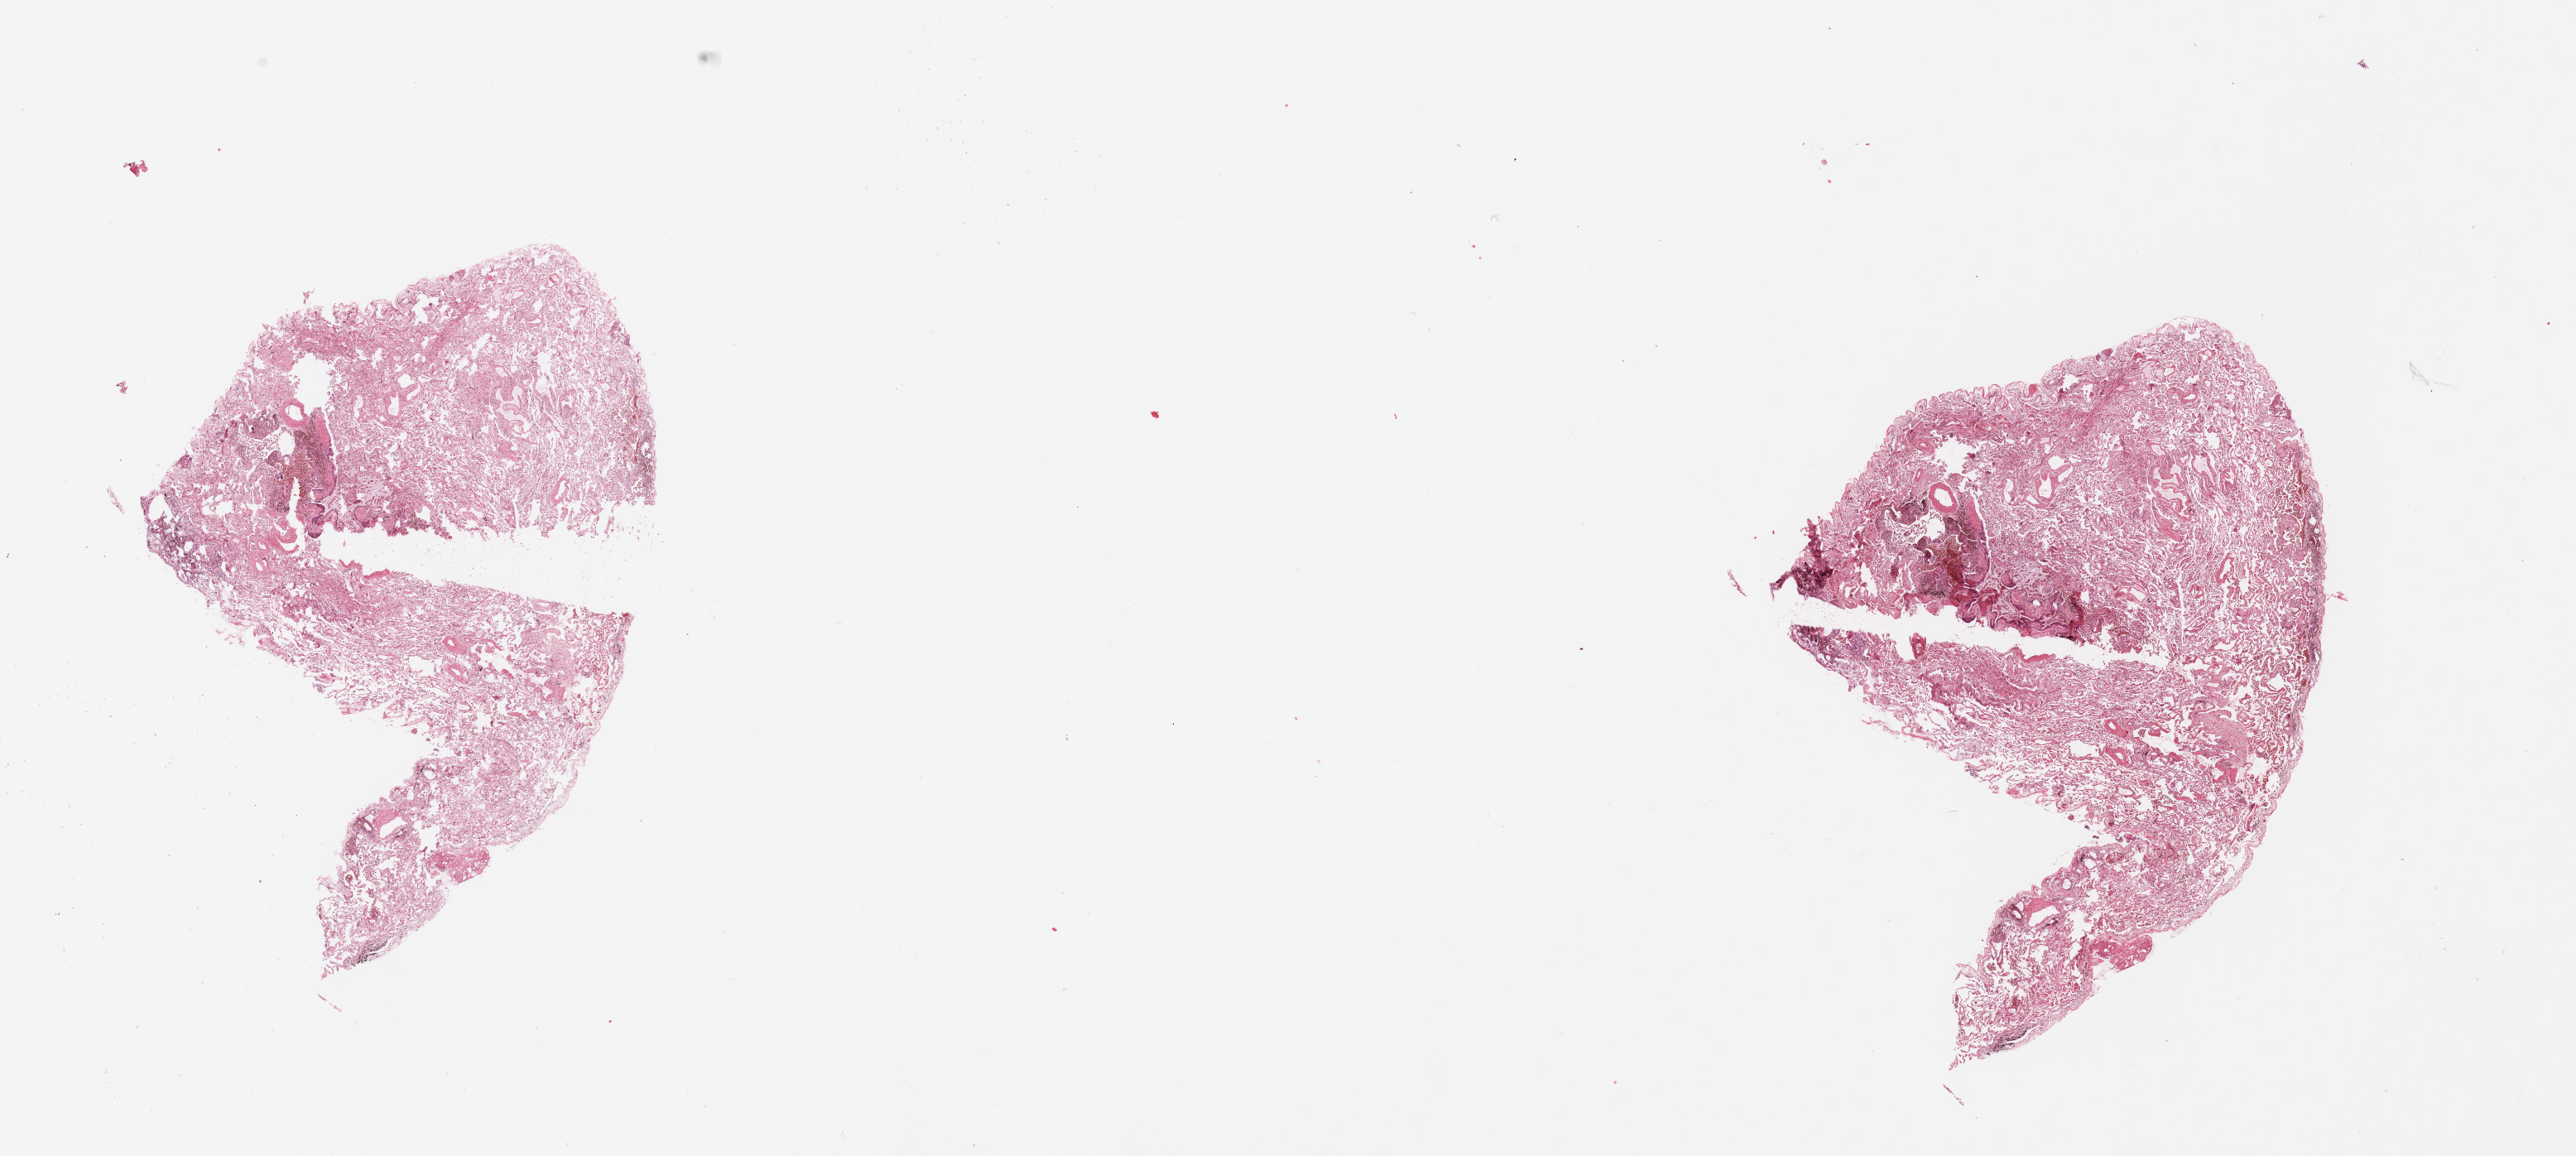
Whole-slide histology image, H&E-stained, whole scanned area (about 24.6 x 11.0 mm, slide scanned at 20x) shown as a low-resolution overview, normal (non-tumour) tissue sample, sampled site: lung. 58-year-old female patient.
This section: normal (non-tumour) tissue from the same patient. Patient diagnosis: Squamous cell carcinoma, NOS.